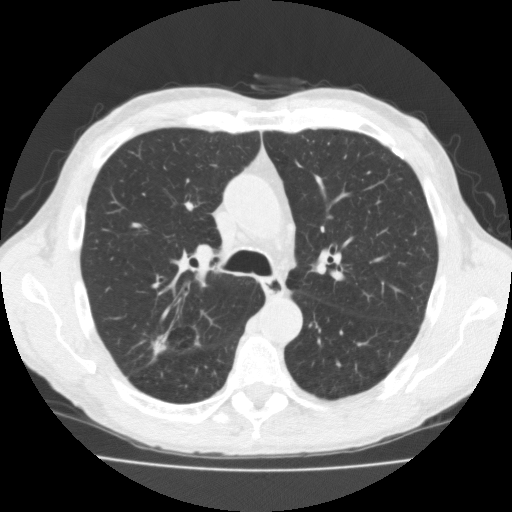
Low-dose screening chest CT, one axial slice. Slice 118 of 181 in the series (ordered by position). Reconstruction kernel FC10. 120 kVp. Lung window (W 1500 / L -600 HU). 2 mm slice thickness. 512 × 512 image matrix.
Structures marked on this image (expert manual segmentation):
- lesion 1 (tumor, upper lobe of right lung): box from (x=152, y=340) to (x=166, y=355) px